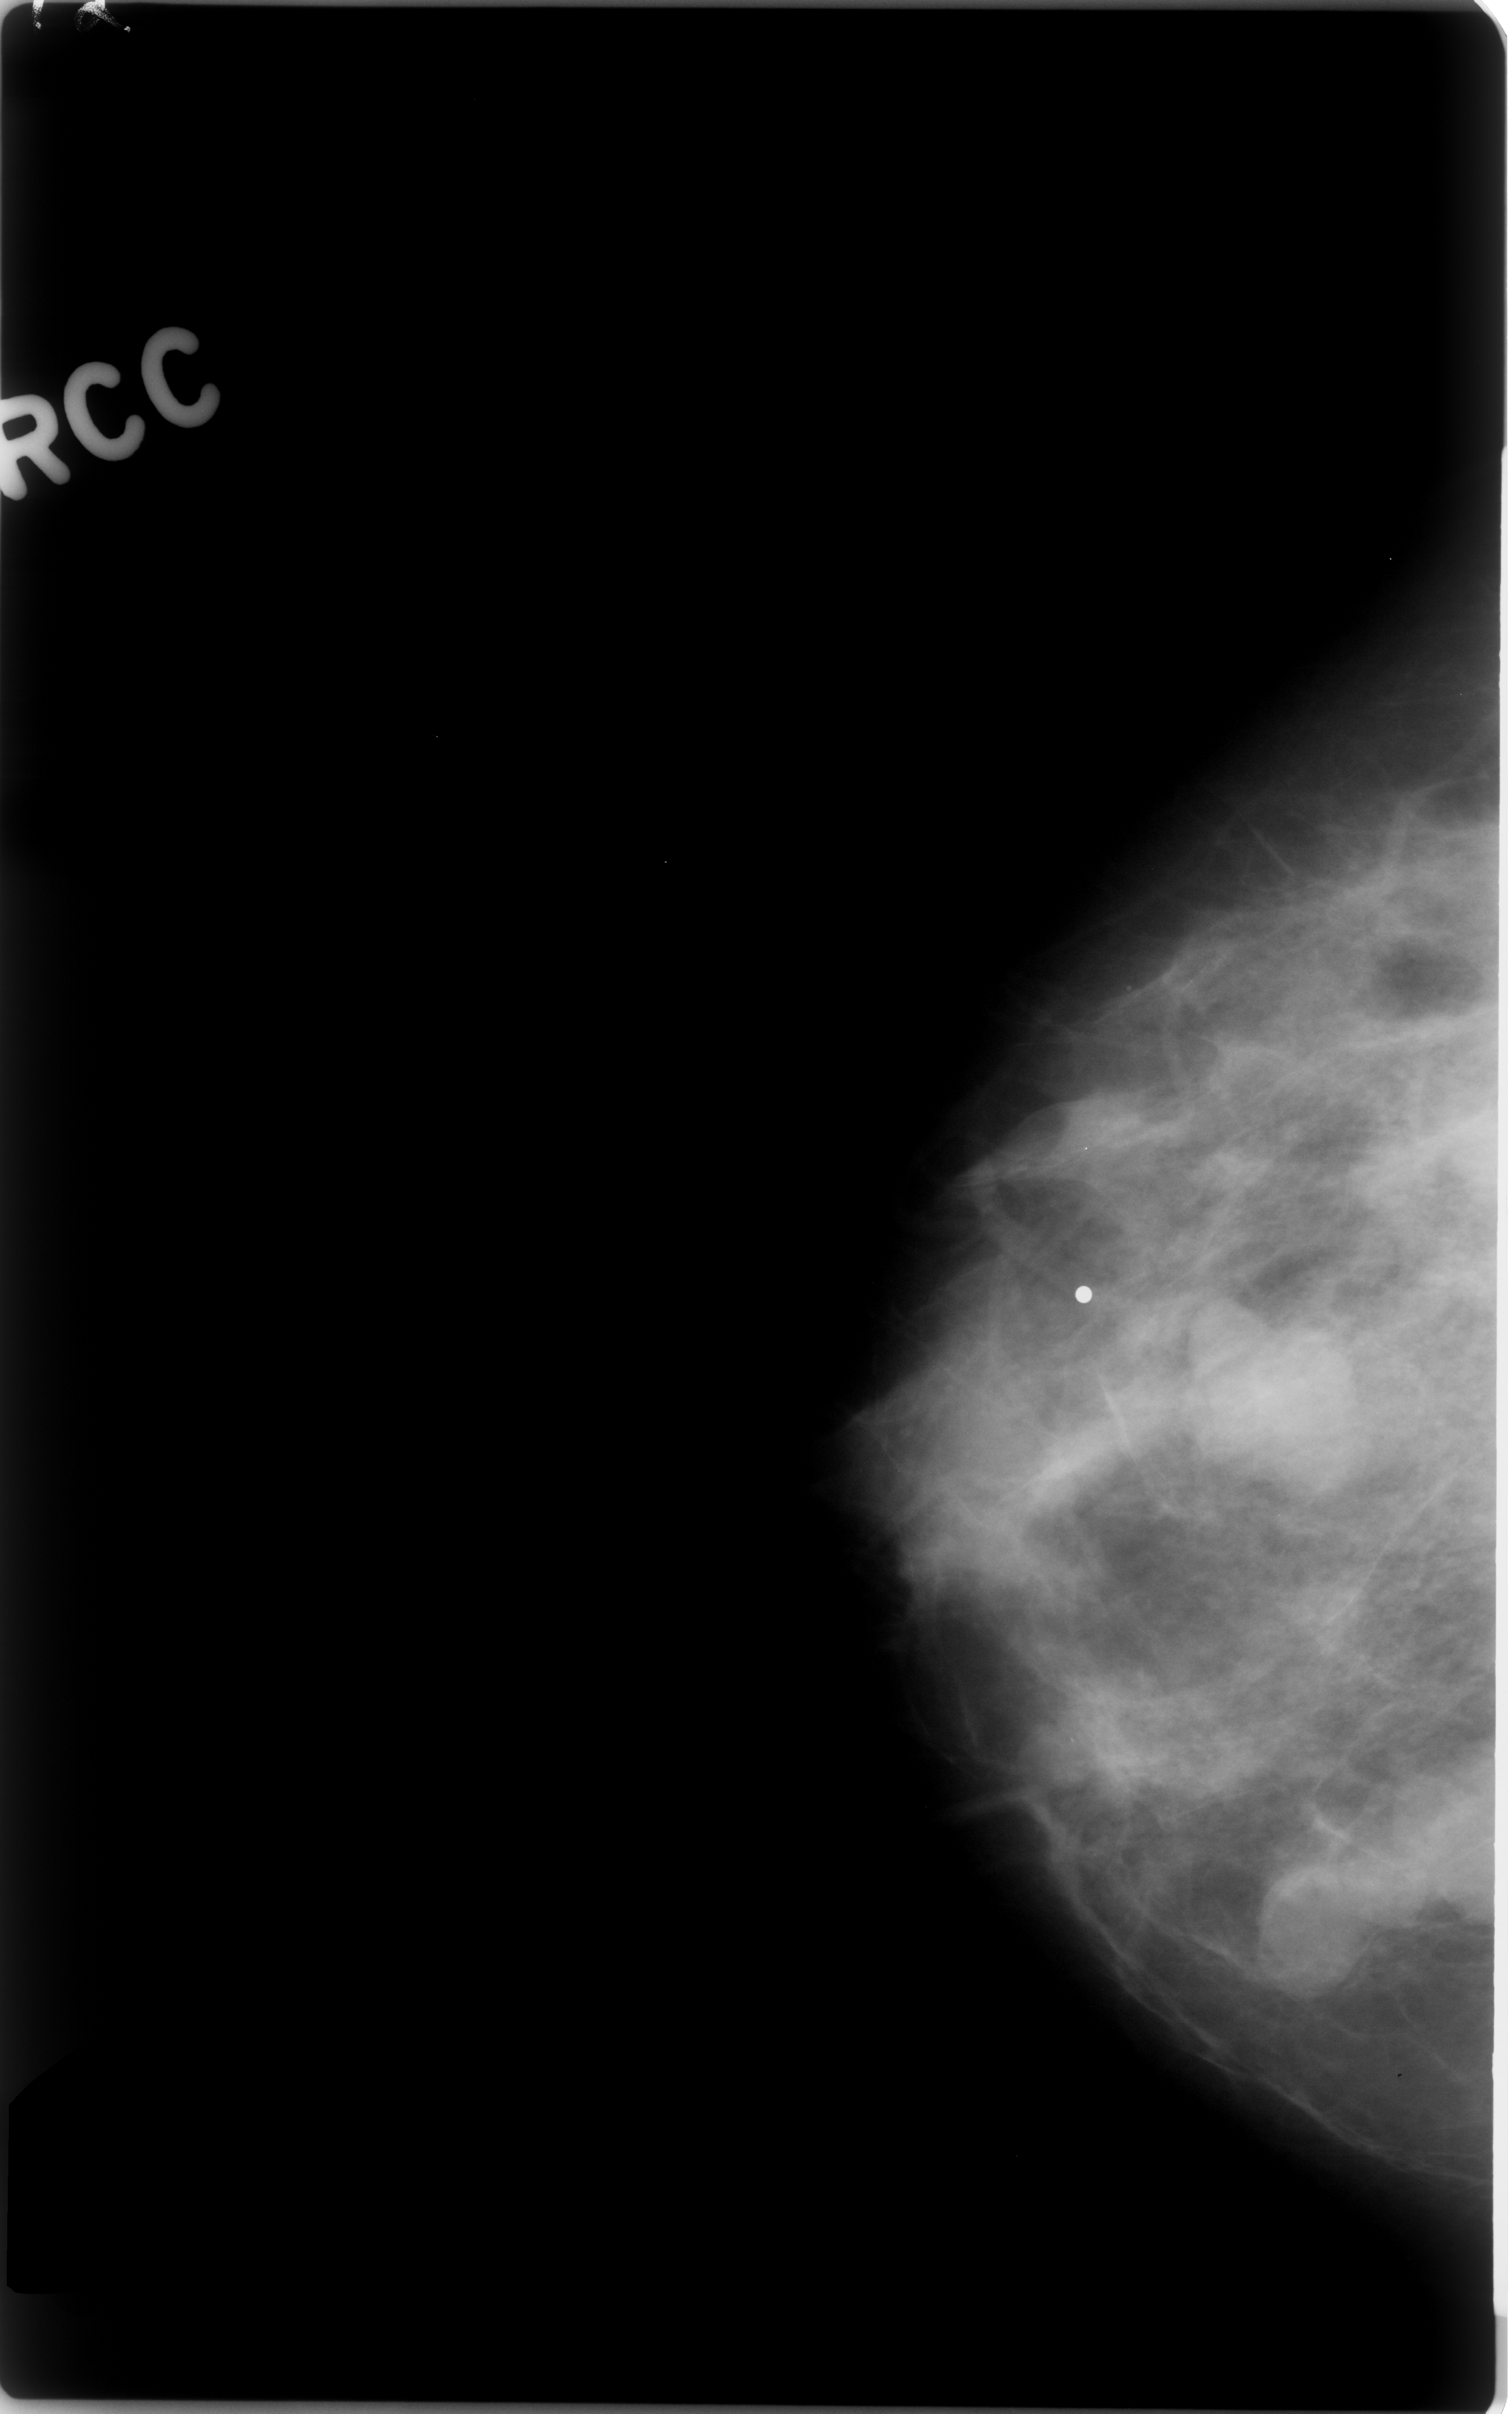
Digitized screen-film mammogram; right breast; CC view; BI-RADS breast density category 3 (scale 1–4).
Marked abnormality: mass, shape lobulated, margins circumscribed; BI-RADS assessment category 4; pathology result (as recorded, not read from the image): benign.